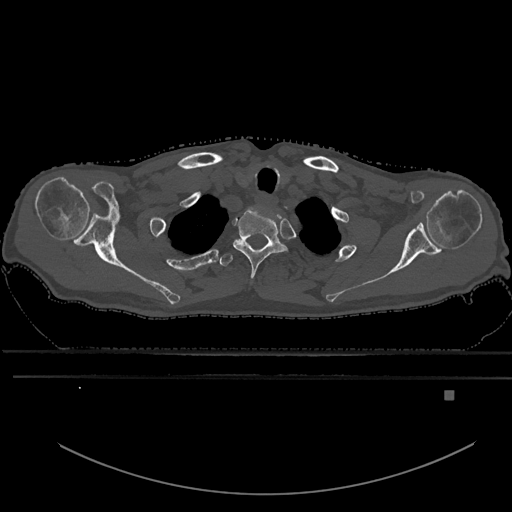
CT including the spine, one axial slice; bone window (W 1800 / L 400 HU); 512 × 512 image matrix, field of view 456 × 456 mm. Patient: male, 82 years. From the clinical record (not read from this slice): primary cancer: prostate.
Outlined on this slice (semi-automatically segmented with operator editing):
- T1 vertebra: bounding box <233,209,287,279> (left, top, right, bottom; pixels)
- T2 vertebra: <219,238,244,266>